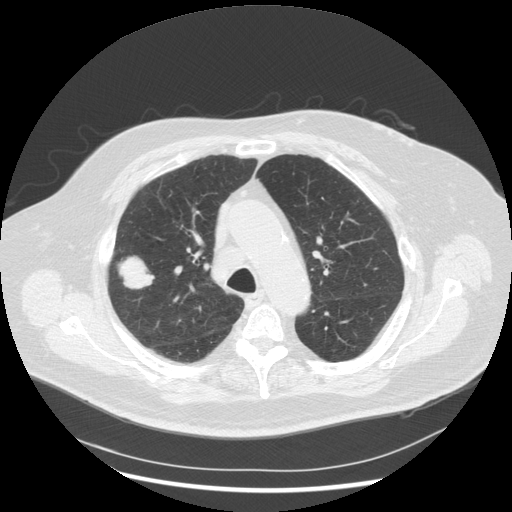
Chest CT (low-dose screening protocol), one axial image. Third screening round (two years after baseline). Lung window (W 1500 / L -600 HU). 2.5 mm slice thickness. Standard (soft-tissue) reconstruction kernel (STANDARD). Slice 198 of 263 in the series. Male, age 72 years at enrolment.
Expert reader's lesion annotation, box from (x=106, y=251) to (x=160, y=300) px. Reader record for this screening exam (exam-level; its link to the box is not recorded): non-calcified nodule or mass ≥4 mm, right upper lobe, 31 × 31 mm, poorly defined margins, soft tissue attenuation, pre-existing on the prior screen: no. Official screen result: positive, other. Later outcome: lung cancer diagnosed 70 days after this screen — squamous cell carcinoma, NOS, right upper lobe, poorly differentiated (G3), stage IIIA (AJCC 6th edition), 19 mm at pathology.